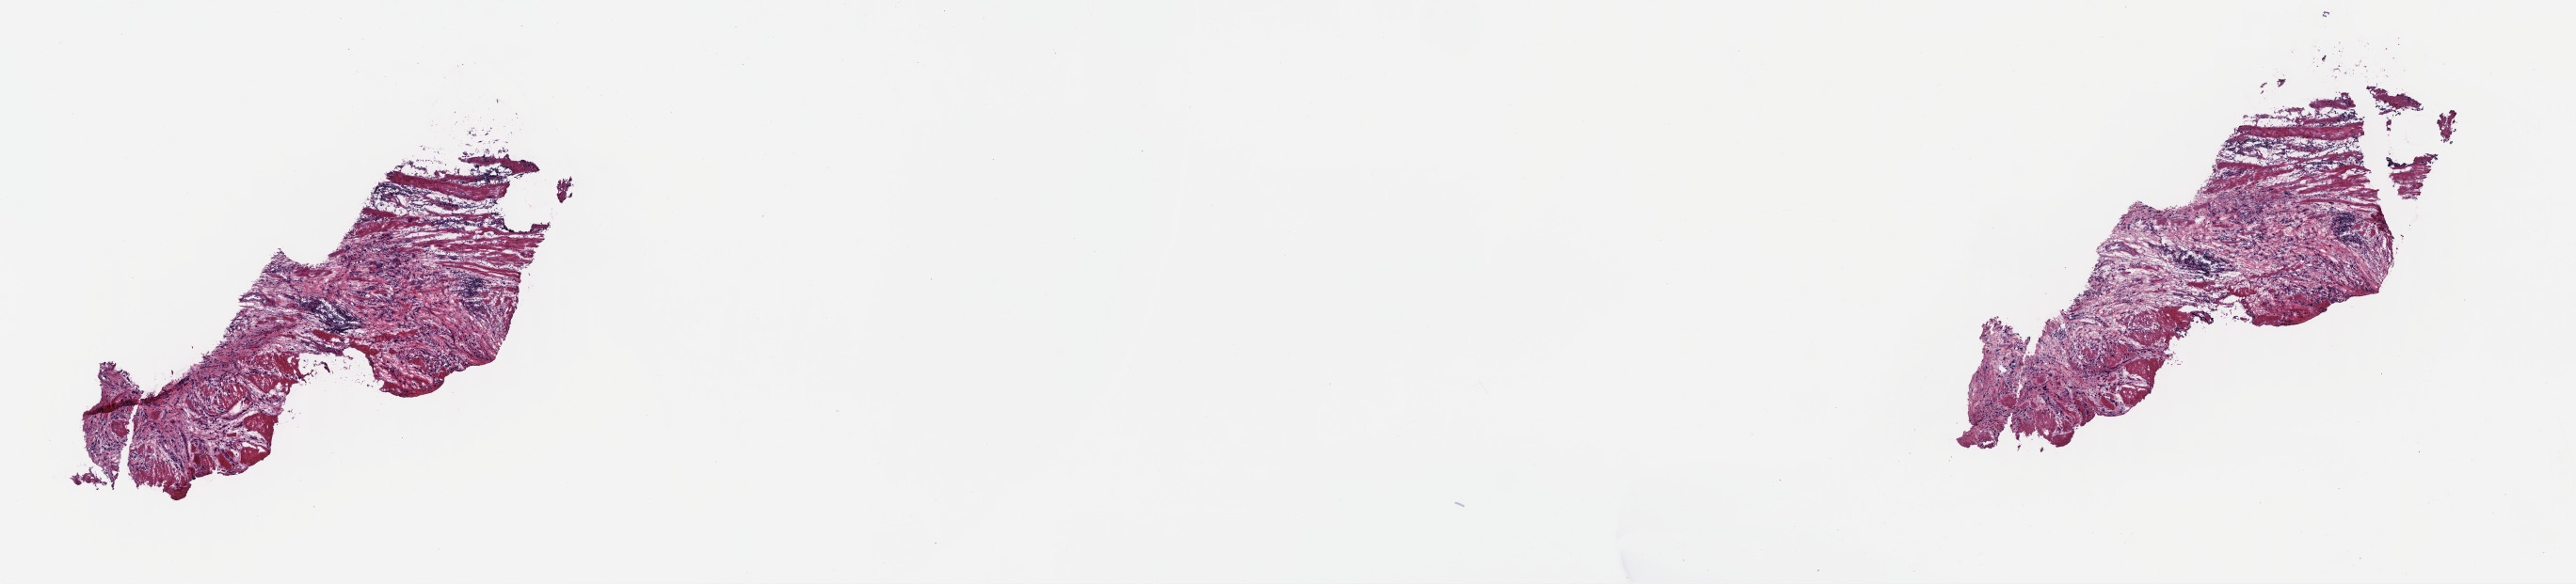
Hematoxylin and eosin (H&E) stained whole-slide image — shown as a low-resolution overview of the whole scanned area (about 21.5 x 4.9 mm), frozen section, primary tumour sample from the stomach. Patient: male, age at initial diagnosis 58 years. Histologic grade: G3 (poorly differentiated). Composition of this section per pathologist review: tumour cells 100%, tumour nuclei 65%, normal cells 0%, stromal cells 0%, necrosis 0%. Inflammatory infiltration, as recorded: lymphocyte infiltration 2%, monocyte infiltration 0%, neutrophil infiltration 0%.
• diagnosis: Carcinoma, diffuse type (gastric antrum)
• AJCC pathologic stage: IIA (7th edition)